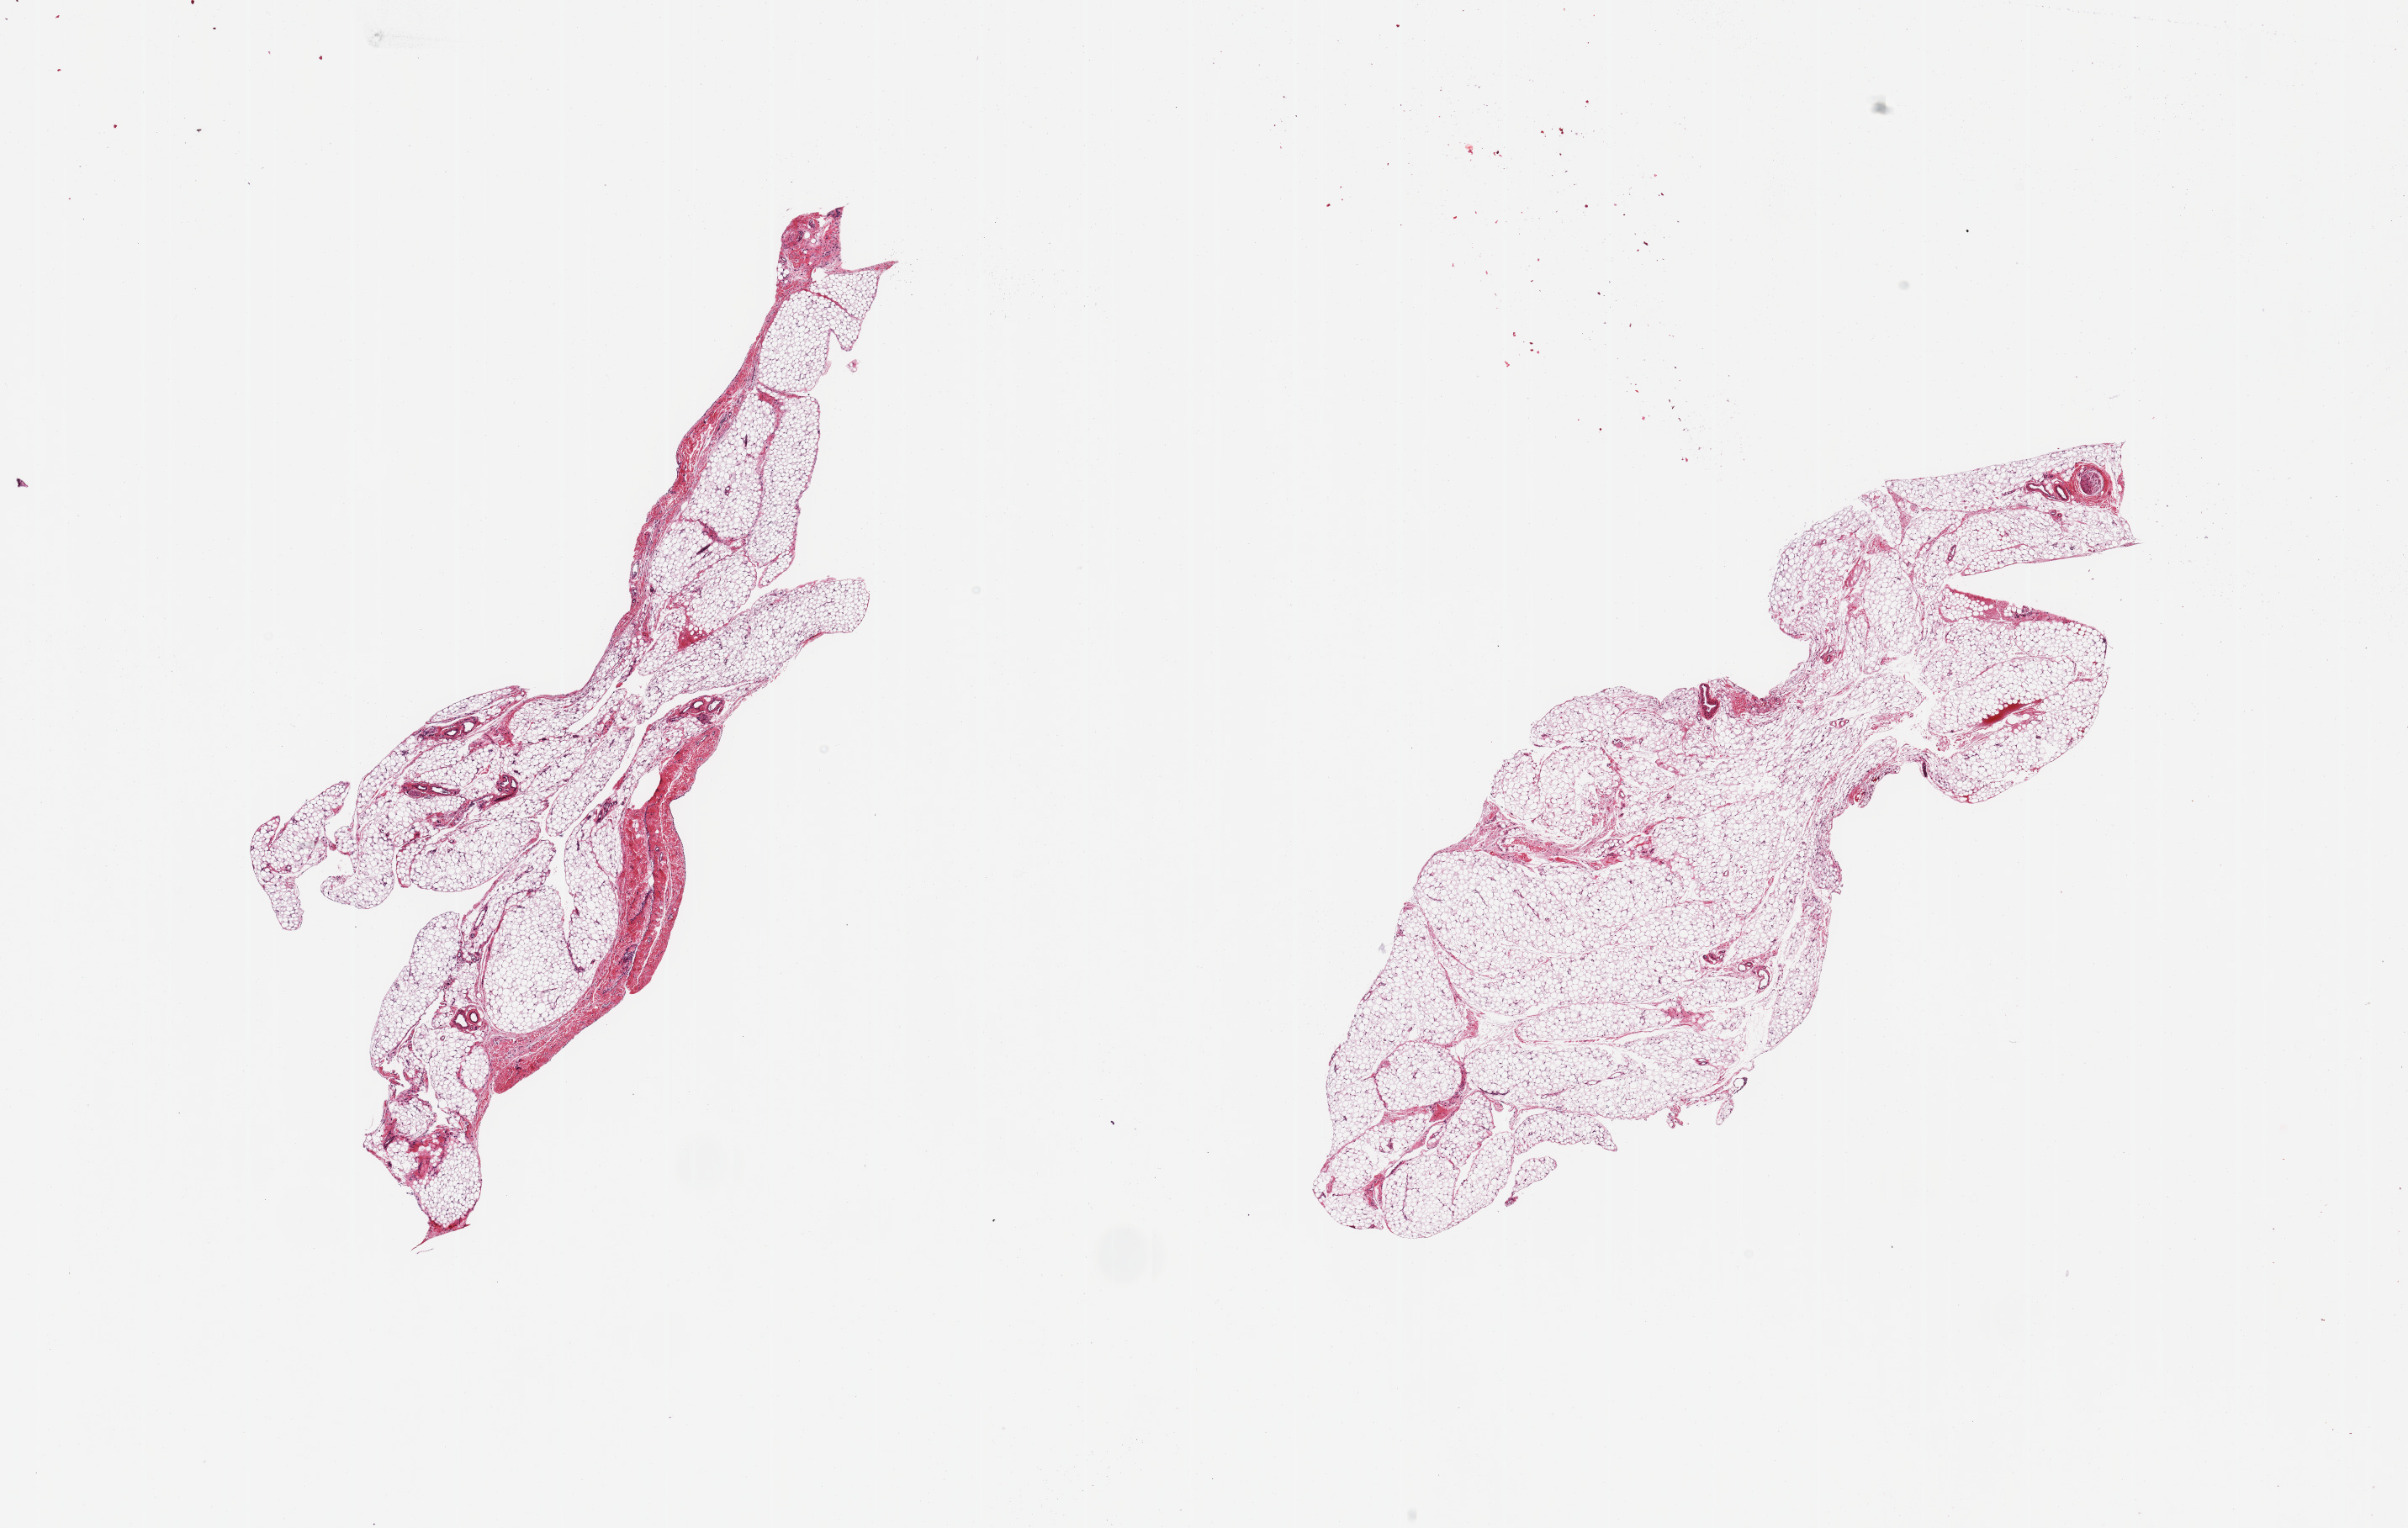
Whole-slide image, haematoxylin and eosin stain, brightfield — low-resolution overview of the scanned area, about 22.6 x 14.4 mm (from a 20x scan); PAXgene-fixed, paraffin-embedded tissue; sampled site (target tissue): omentum; donor tissue sample. Female donor.
* reviewer comment on this tissue sample: 2 pieces; 1 with 10% fibrous content, other with <5%